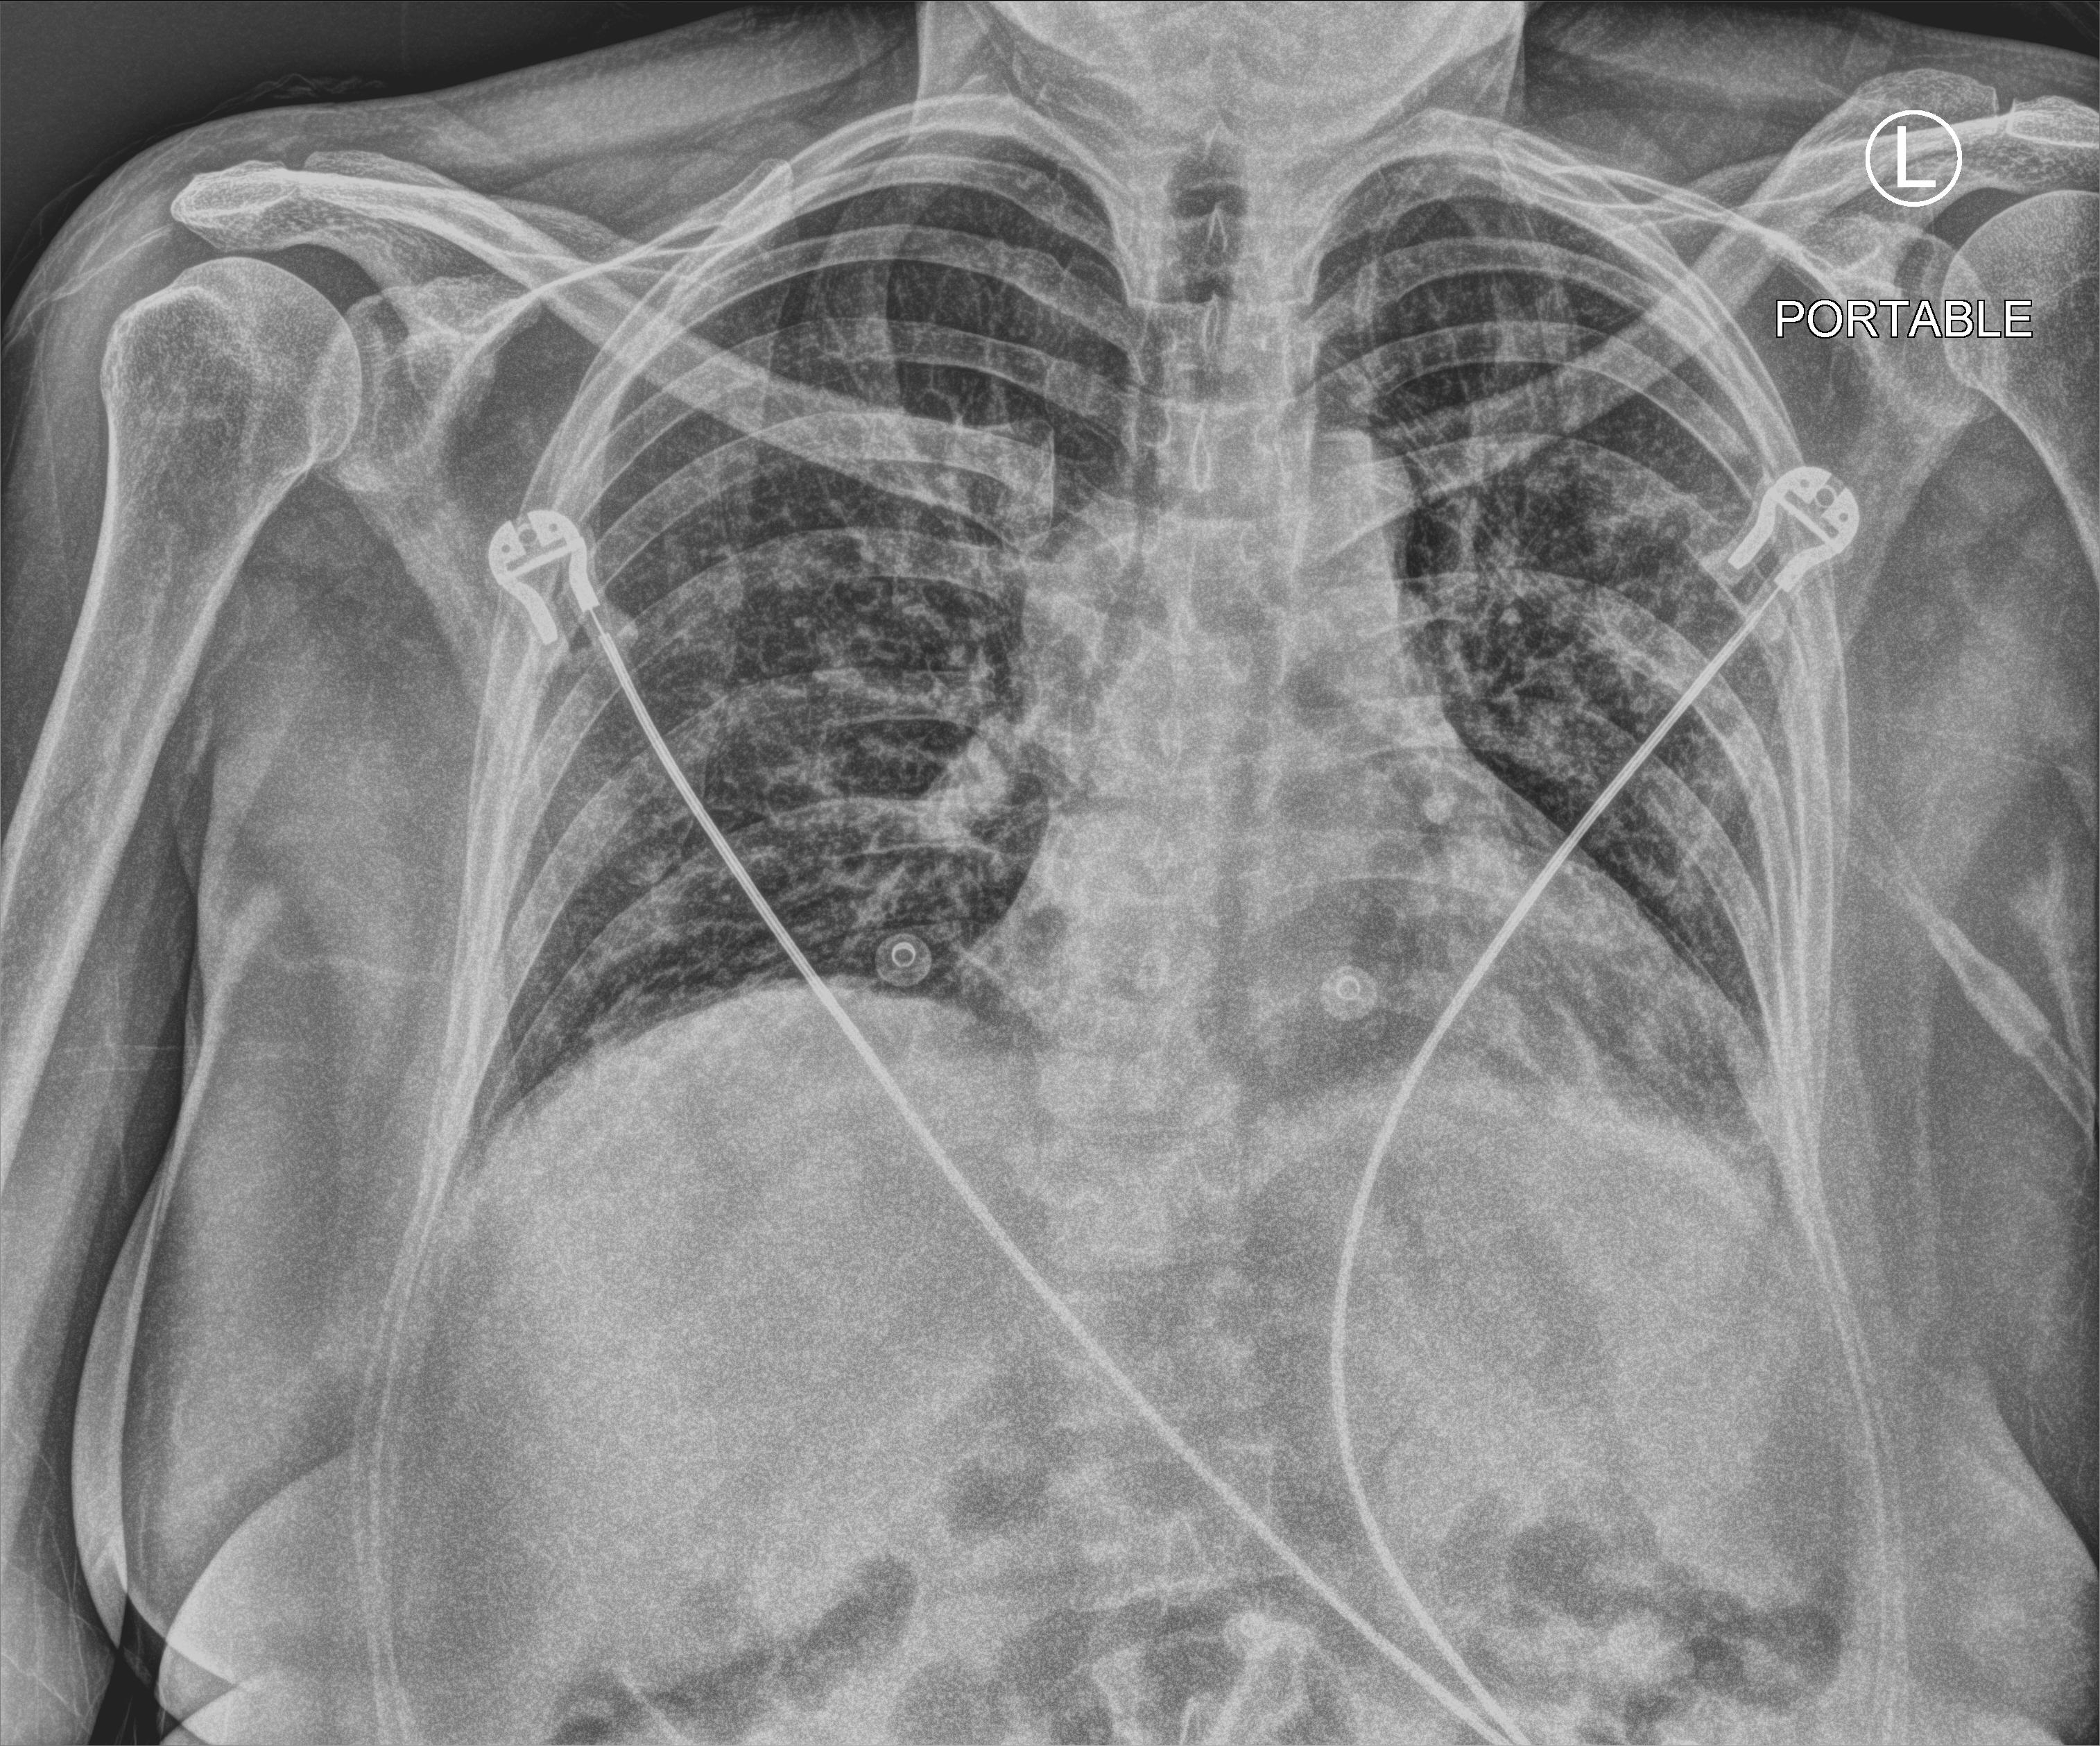
Chest X-ray (portable), anteroposterior (AP) projection. Patient hospitalised with COVID-19; female, aged 18–59 years.
From the hospital-stay record, not from the radiograph (when in the stay this image was taken is not recorded): admitted to intensive care during this hospital stay: no.